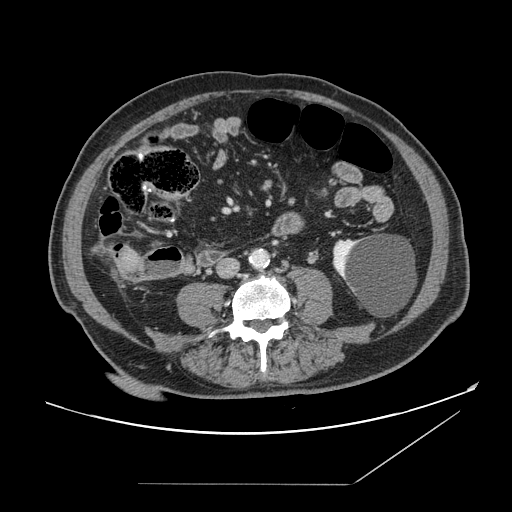
Contrast-enhanced abdominal CT, one axial slice; slice 21 of 166 in the series (ordered by position); soft-tissue window (W 400 / L 40 HU); 2.5 mm slice thickness; 512 × 512 image matrix, field of view 416 × 416 mm. Male patient, age 80 years. Case-level facts recorded for this patient, not image findings: diagnosis: colorectal cancer liver metastases, imaged before liver resection; multiple liver metastases: no; largest metastasis: 2.2 cm; disease in both lobes: no.
Structures marked on this image (expert manual segmentation):
- liver: bounding box (x1, y1, x2, y2) in pixels: (116, 247, 143, 276)